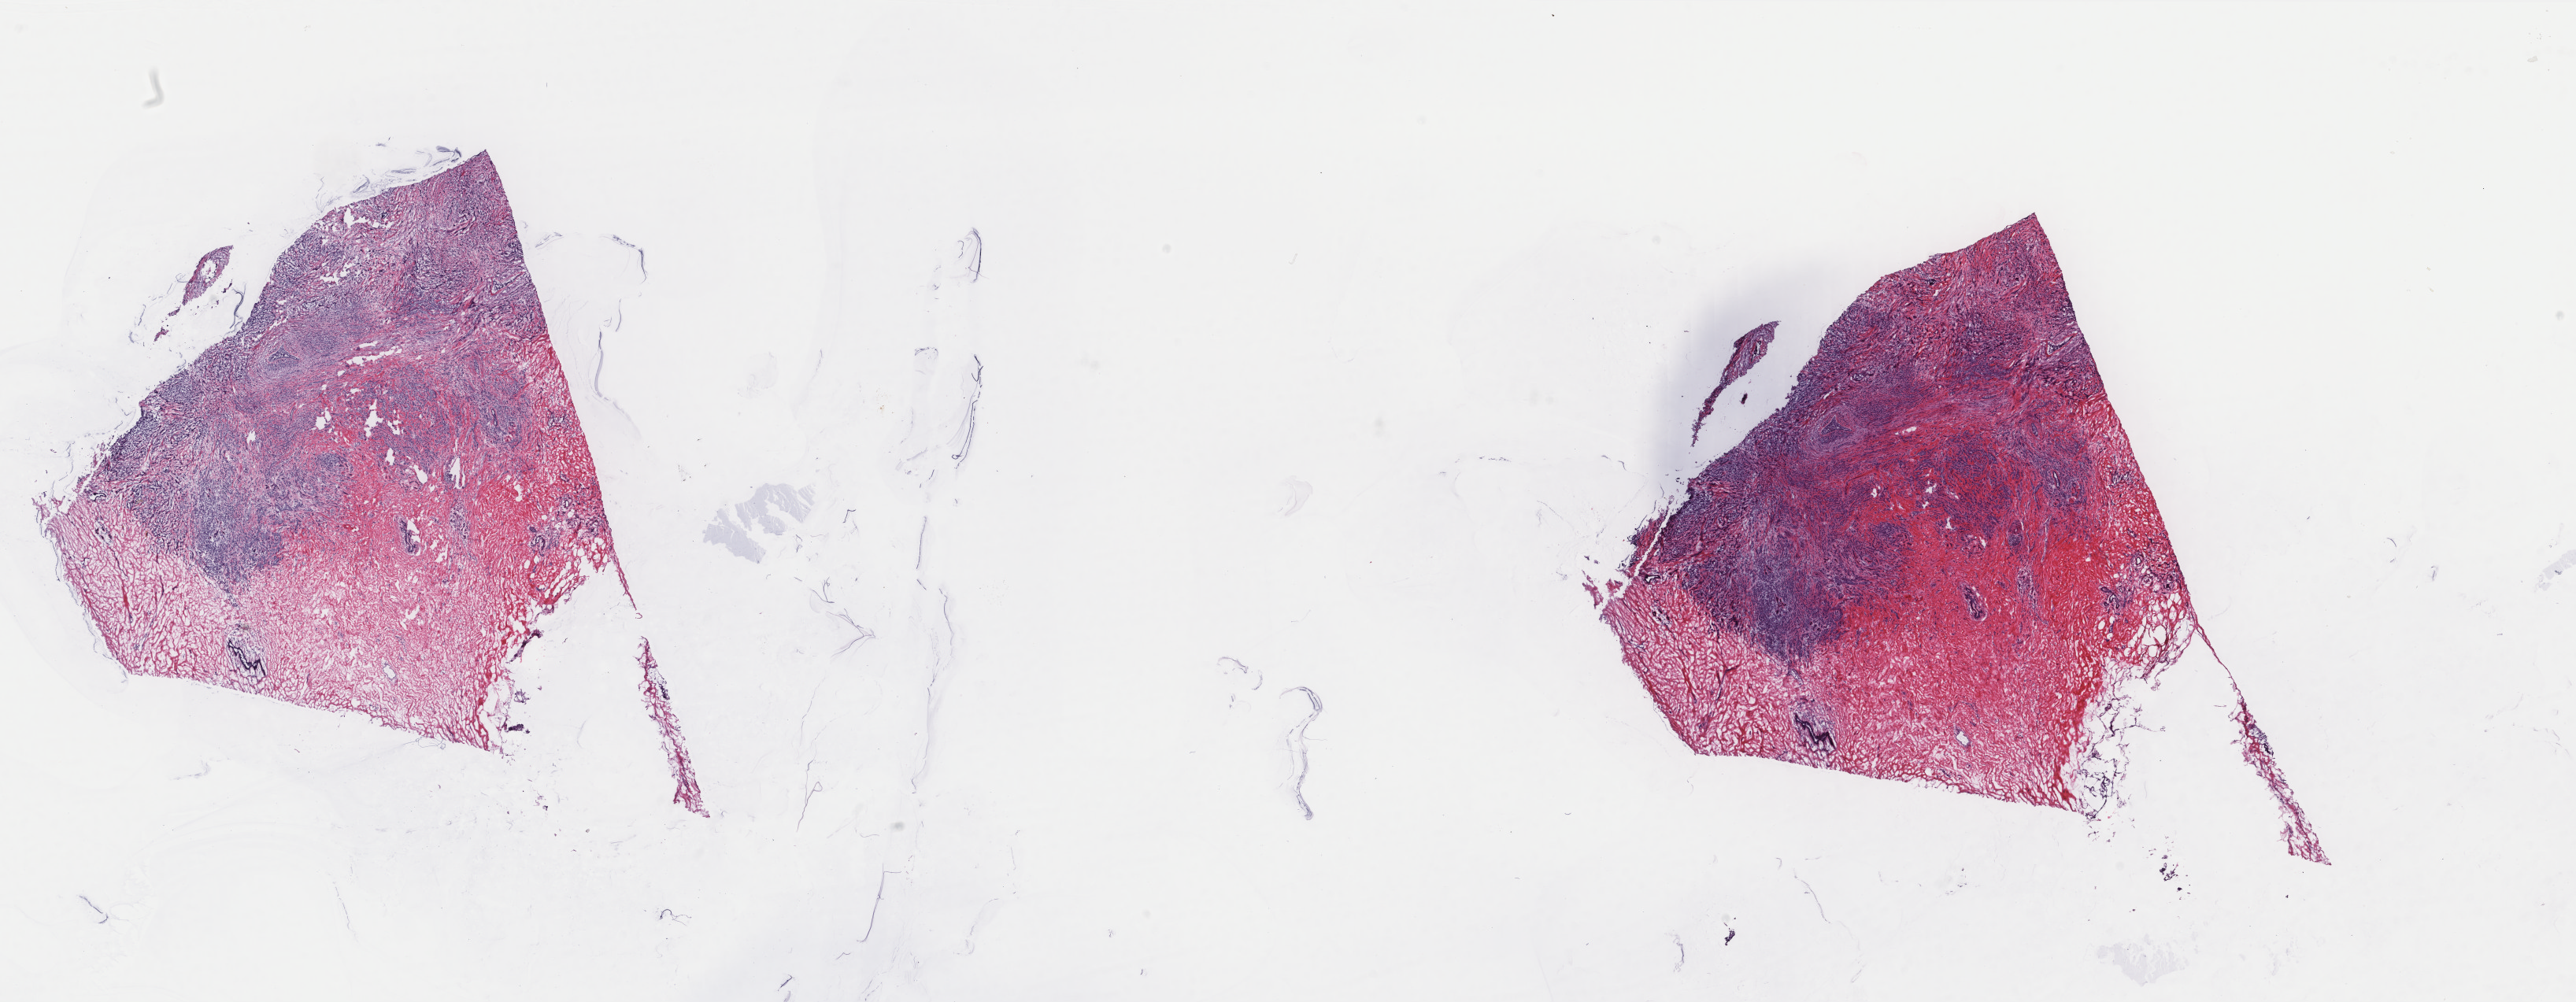
Digitized H&E-stained tissue section (whole slide), shown as a low-resolution overview of the whole scanned area (about 26.0 x 10.1 mm); frozen section from the top of the tissue portion; breast, primary tumour sample. Female, age 70 years at initial diagnosis. Pathologist review of this section (percent, as recorded): tumour cells 65%, tumour nuclei 80%, normal cells 5%, stromal cells 30%, necrosis 0%. Infiltration values recorded for this section: lymphocyte infiltration 0%, monocyte infiltration 0%, neutrophil infiltration 0%.
Lymph nodes positive (case pathology): 0 of 5 examined. Histologic diagnosis: Lobular carcinoma, NOS. AJCC pathologic stage: I (6th edition).